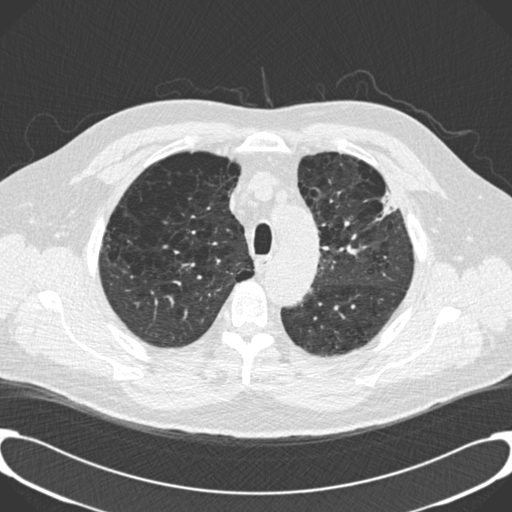
Low-dose screening chest CT, one axial slice; slice 154 of 189 in the series (ordered by position); 120 kVp; lung window (W 1500 / L -600 HU); 2 mm slice thickness; 512 × 512 image matrix, field of view 380 × 380 mm.
Annotated regions visible in this slice (outlined manually by an expert reader):
- lesion 1 (tumor, upper lobe of left lung): bounding box (x1, y1, x2, y2) in pixels: (377, 190, 399, 220)